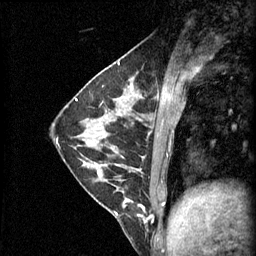
Breast MRI (dynamic contrast-enhanced), one sagittal slice. Position 20 of 60 along the scan axis. 3 images stored at this slice position (order not interpretable as contrast timing). 1.5 T. TE 4.2 ms, TR 11 ms. 2.1 mm slice thickness. 256 × 256 image matrix, field of view 180 × 180 mm. Patient: female, 29 years.
Structures marked on this image (semi-automatic segmentation, software-assisted and operator-edited):
- analysis volume of interest (the breast-tissue region the enhancement analysis was run in; not a lesion): bounding box [x1, y1, x2, y2] px = [93, 164, 153, 229]
- tumour enhancement mask (voxels above the 70 % enhancement threshold inside the analysis volume of interest): [124, 198, 151, 219]